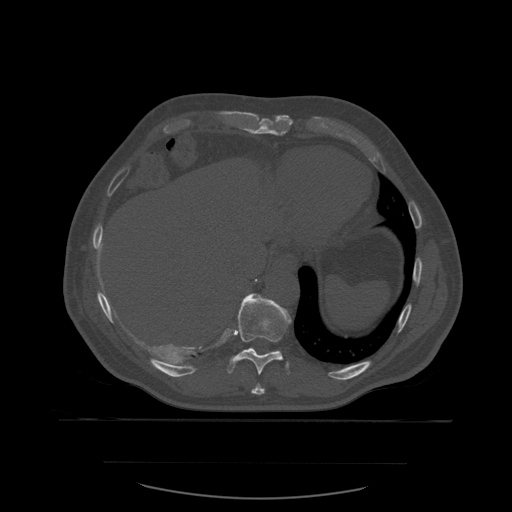
CT including the spine, one axial slice; position 317 of 590 along the scan axis; bone window (W 1800 / L 400 HU); 1.25 mm slice thickness; 512 × 512 image matrix, field of view 479 × 479 mm. Patient age 71 years. Case-level facts recorded for this patient, not image findings: primary cancer: lung; vertebrae with lytic lesions (as recorded): T1, T2, L5, S1.
Outlined on this slice (semi-automatically segmented with operator editing):
- T10 vertebra: bounding box <227,294,292,375> (left, top, right, bottom; pixels)
- T11 vertebra: <246,349,277,352>
- T9 vertebra: <252,384,266,395>